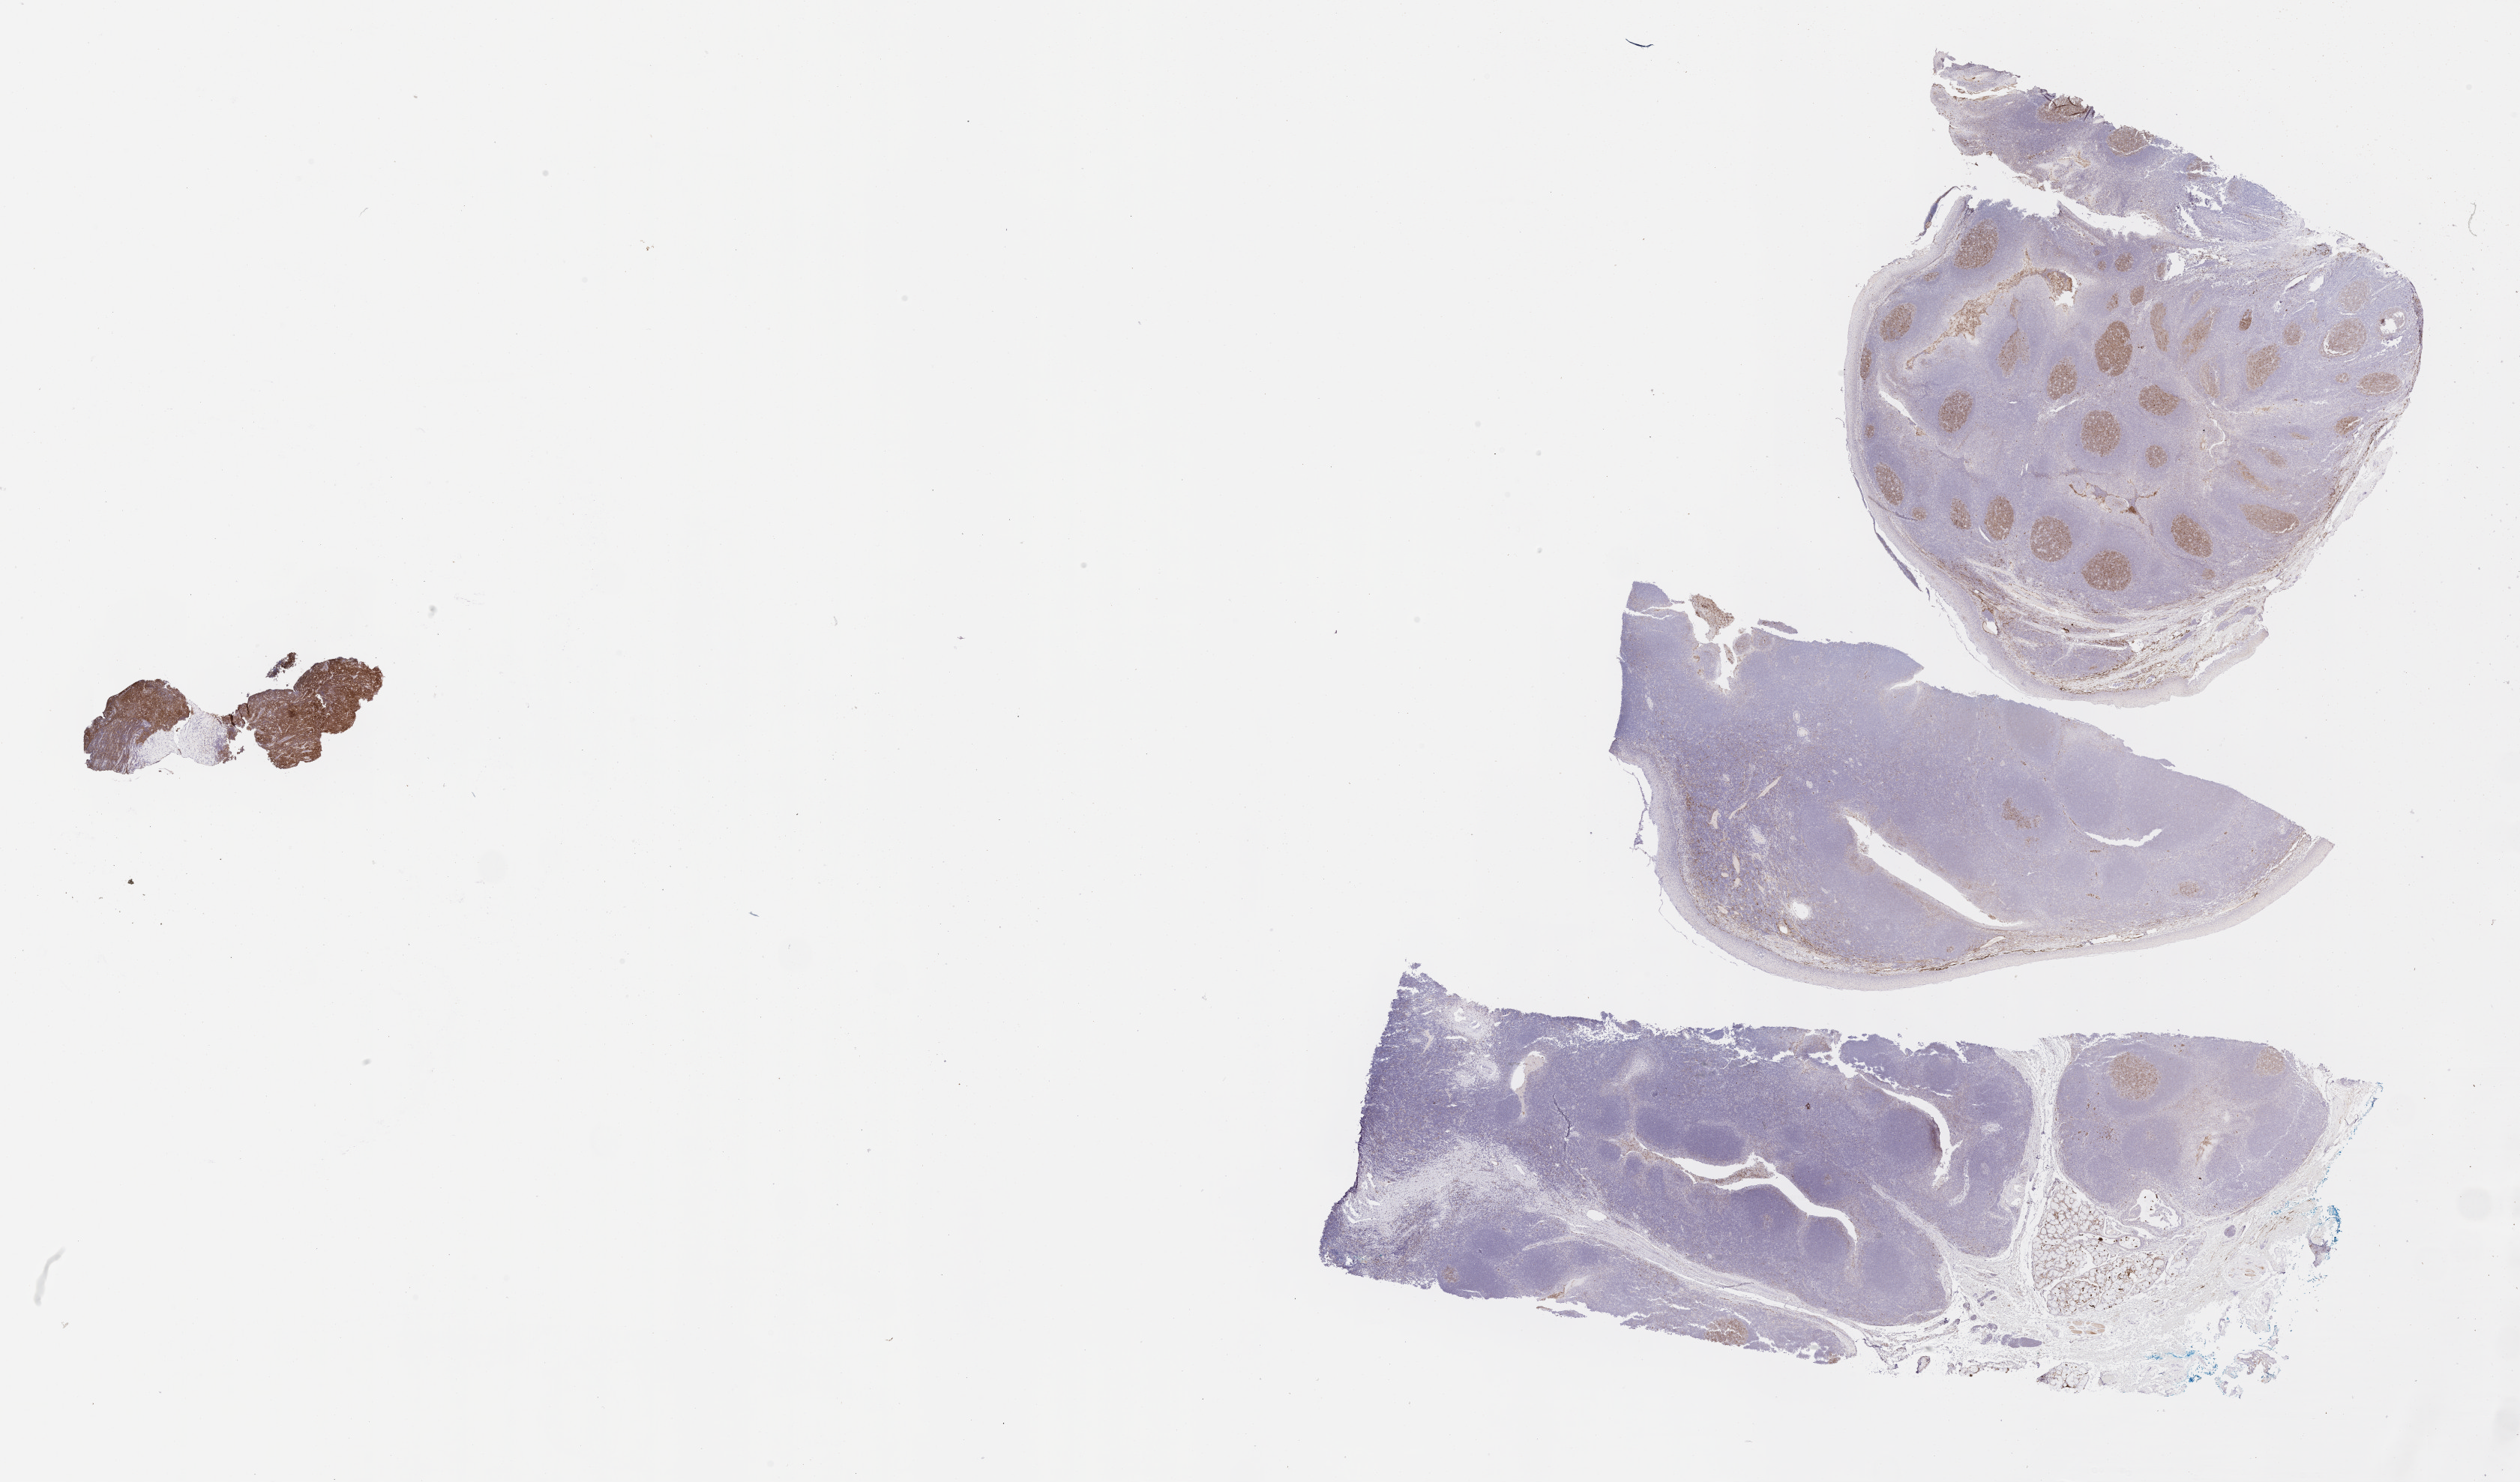
Whole-slide image, immunohistochemical stain for CD10, whole scanned area (about 27.2 x 16.0 mm) shown as a low-resolution overview; tumor tissue. Male patient, 15 years old.
Histologic diagnosis: Burkitt lymphoma, NOS.